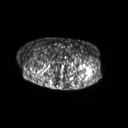
FDG PET of an extremity soft-tissue mass (from a PET/CT study), one axial slice; slice 262 of 267 in the series (ordered by position); 128 × 128 image matrix. Patient: female, 62 years. From the clinical record (not read from this slice): histological type: undifferentiated – high grade; grade: high; site of the primary tumour: left thigh.
Structures marked on this image (expert contour drawn on MRI and transferred to this co-registered scan by the dataset authors):
- gross tumour volume including surrounding oedema: box from (x=90, y=72) to (x=91, y=74) px